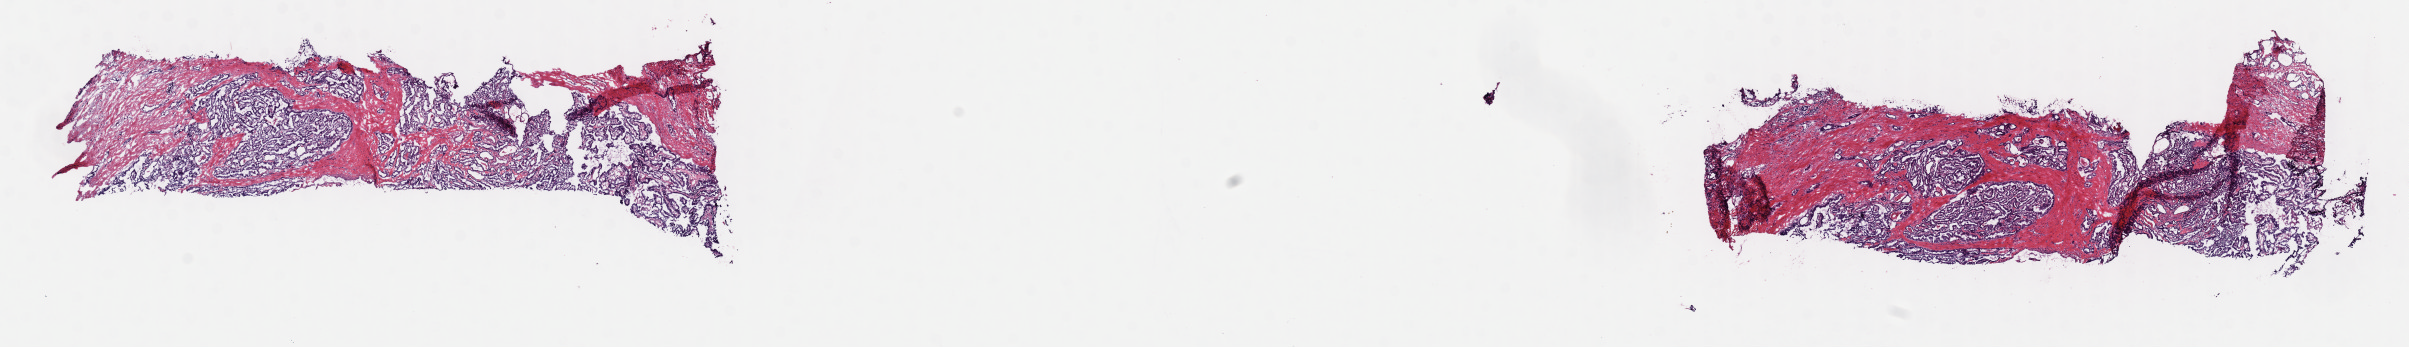
Digitized H&E-stained tissue section (whole slide) — a low-resolution overview of the entire scanned area, about 19.0 x 2.7 mm (from a 40x scan), frozen section from the top of the tissue portion, sample: primary tumour, thyroid. Patient: female, age at initial diagnosis 47 years. Composition of this section per pathologist review: tumour cells 60%, tumour nuclei 80%, normal cells 0%, stromal cells 40%, necrosis 0%. Inflammatory infiltration, as recorded: lymphocyte infiltration 1%, monocyte infiltration 0%, neutrophil infiltration 0%.
• lymph nodes positive (case pathology): 0 of 3 examined
• histologic diagnosis: Papillary carcinoma, columnar cell (thyroid gland)
• AJCC pathologic stage: I